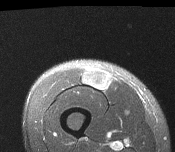
MRI of an extremity soft-tissue mass, one axial slice. Position 41 of 116 along the scan axis. T2-weighted fat-saturated. MR volume resampled by the dataset authors to the PET/CT grid (not the native acquisition matrix). 3.27 mm slice thickness. 175 × 152 image matrix, field of view 171 × 148 mm. Male patient. From the clinical record (not read from this slice): histological type: pleiomorphic leiomyosarcoma; grade: intermediate; site of the primary tumour: right thigh.
Structures marked on this image (expert contour drawn on MRI and transferred to this co-registered scan by the dataset authors):
- gross tumour volume including surrounding oedema: bounding box <83,70,109,91> (left, top, right, bottom; pixels)